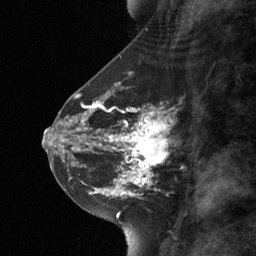
Breast MRI (dynamic contrast-enhanced), one sagittal slice; slice 30 of 64 in the series (ordered by position); dynamic contrast-enhanced study with each time point stored as its own series, time point 2 of 3 at this slice position (early post-contrast, ordered by acquisition time); 1.5 T; TE 4.8 ms, TR 27 ms; 2 mm slice thickness; 256 × 256 image matrix. Patient: female, 42 years. Case-level facts recorded for this patient, not image findings: setting: breast cancer imaged before/during neoadjuvant chemotherapy; receptor status: triple-negative.
Annotated regions visible in this slice (semi-automatically segmented with operator editing):
- analysis volume of interest (the breast-tissue region the enhancement analysis was run in; not a lesion): bounding box (x1, y1, x2, y2) in pixels: (111, 104, 170, 178)
- tumour enhancement mask (voxels above the 90 % enhancement threshold inside the analysis volume of interest): (111, 113, 166, 178)